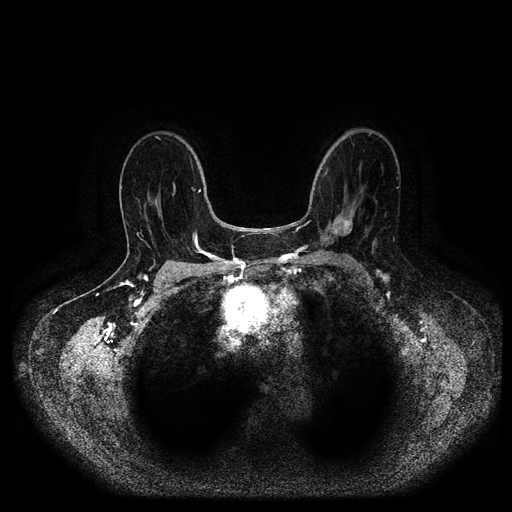
Breast MRI (dynamic contrast-enhanced, multi-phase), one axial slice; position 57 of 116 along the scan axis; dynamic contrast-enhanced series, time point 2 of 5 at this slice position (early post-contrast); 1.5 T; TE 2.6 ms, TR 5.2 ms; 512 × 512 image matrix, field of view 380 × 380 mm. Patient: female, 69 years.
Outlined on this slice (semi-automatic segmentation, software-assisted and operator-edited):
- breast lesion (labelled 'tumour' in the annotation; benign lesions carry a separate 'benign' label): bounding box [x1, y1, x2, y2] px = [329, 211, 355, 235]